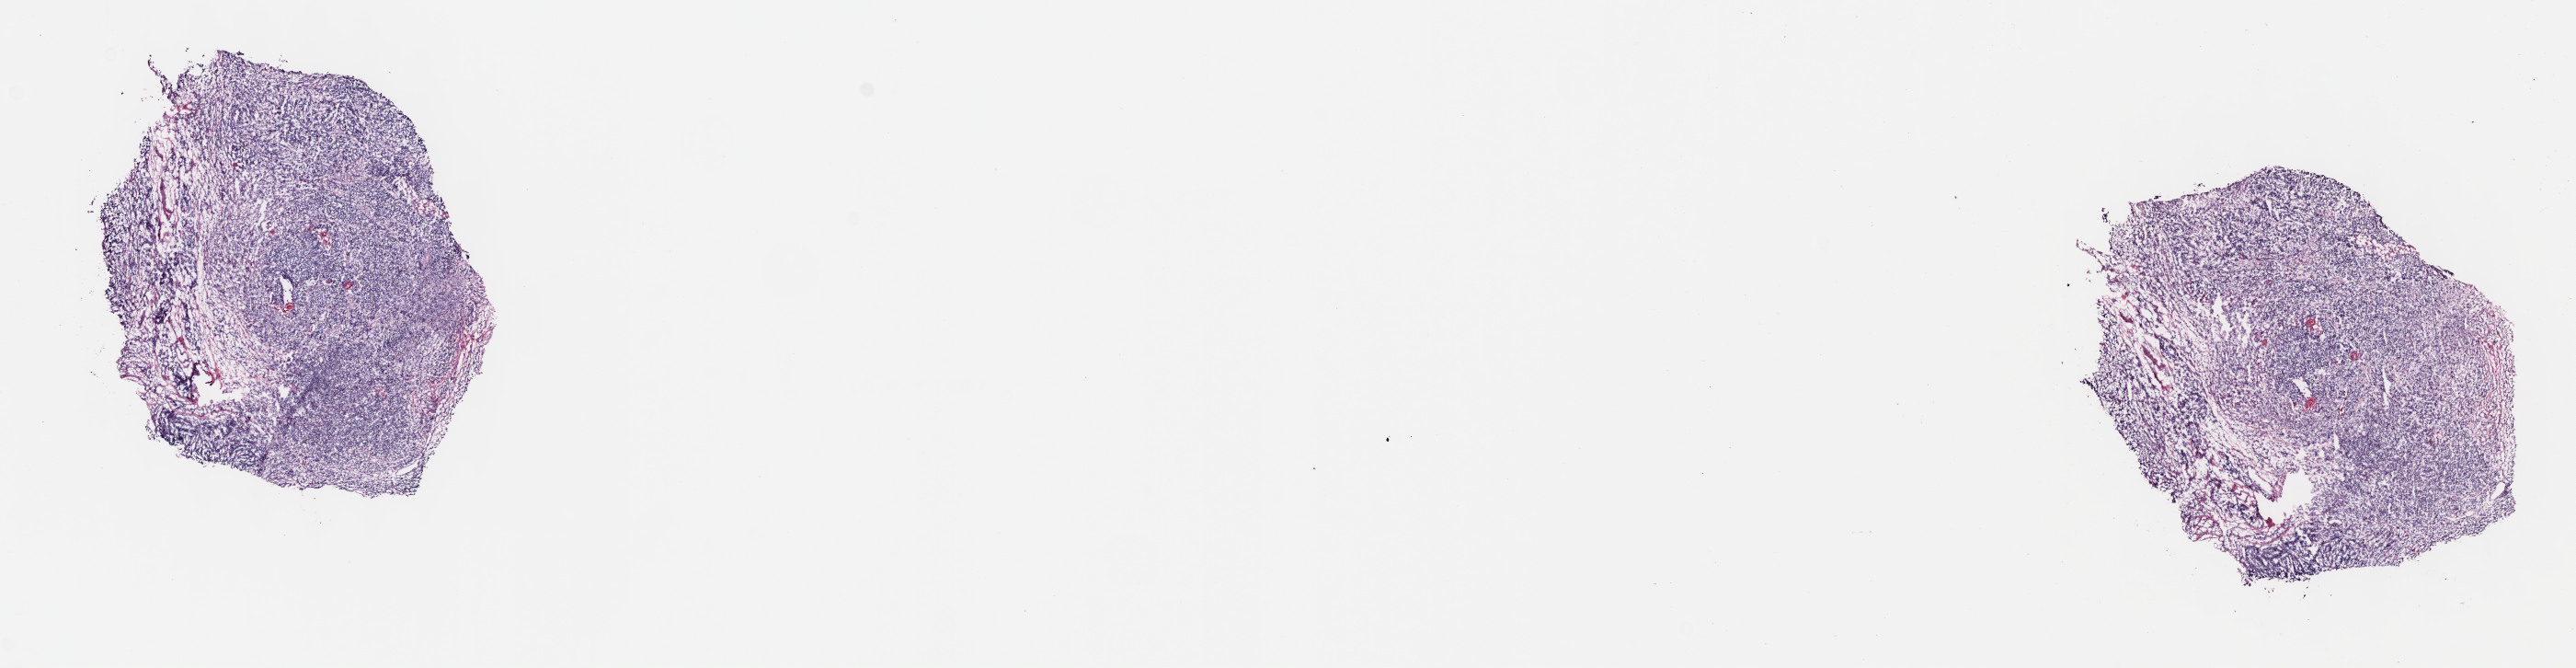
Digitized Hematoxylin and eosin (H&E) stained tissue section (whole slide), shown as a low-resolution overview of the whole scanned area (about 22.7 x 5.9 mm, slide scanned at 40x); frozen section from the top of the tissue portion; primary tumour sample from the head and neck. Patient: male, age at initial diagnosis 56 years. Histologic grade: G3 (poorly differentiated). Slide review estimates, as recorded: tumour cells 100%, tumour nuclei 80%, normal cells 0%, stromal cells 0%, necrosis 0%. Infiltration values recorded for this section: lymphocyte infiltration 3%, monocyte infiltration 0%, neutrophil infiltration 0%.
AJCC pathologic stage: IVA (7th edition). Laterality: right. TNM: T2 N2b M0. Histologic diagnosis: Squamous cell carcinoma, large cell, nonkeratinizing, NOS (tonsil, NOS).